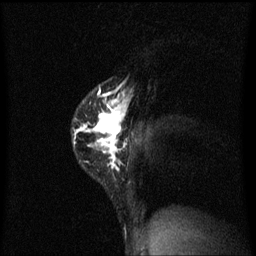
Breast MRI (dynamic contrast-enhanced), one sagittal slice. Slice 45 of 60 in the series (ordered by position). Dynamic contrast-enhanced series, image 2 of 3 at this slice position (ordered by acquisition). 1.5 T. TE 4.2 ms, TR 8.4 ms. 2 mm slice thickness. 256 × 256 image matrix, field of view 200 × 200 mm. Patient: female, 40 years.
Structures marked on this image (semi-automatic segmentation, software-assisted and operator-edited):
- analysis volume of interest (the breast-tissue region the enhancement analysis was run in; not a lesion): box from (x=73, y=78) to (x=130, y=171) px
- tumour enhancement mask (voxels above the 70 % enhancement threshold inside the analysis volume of interest): (x=74, y=86)–(x=130, y=171)